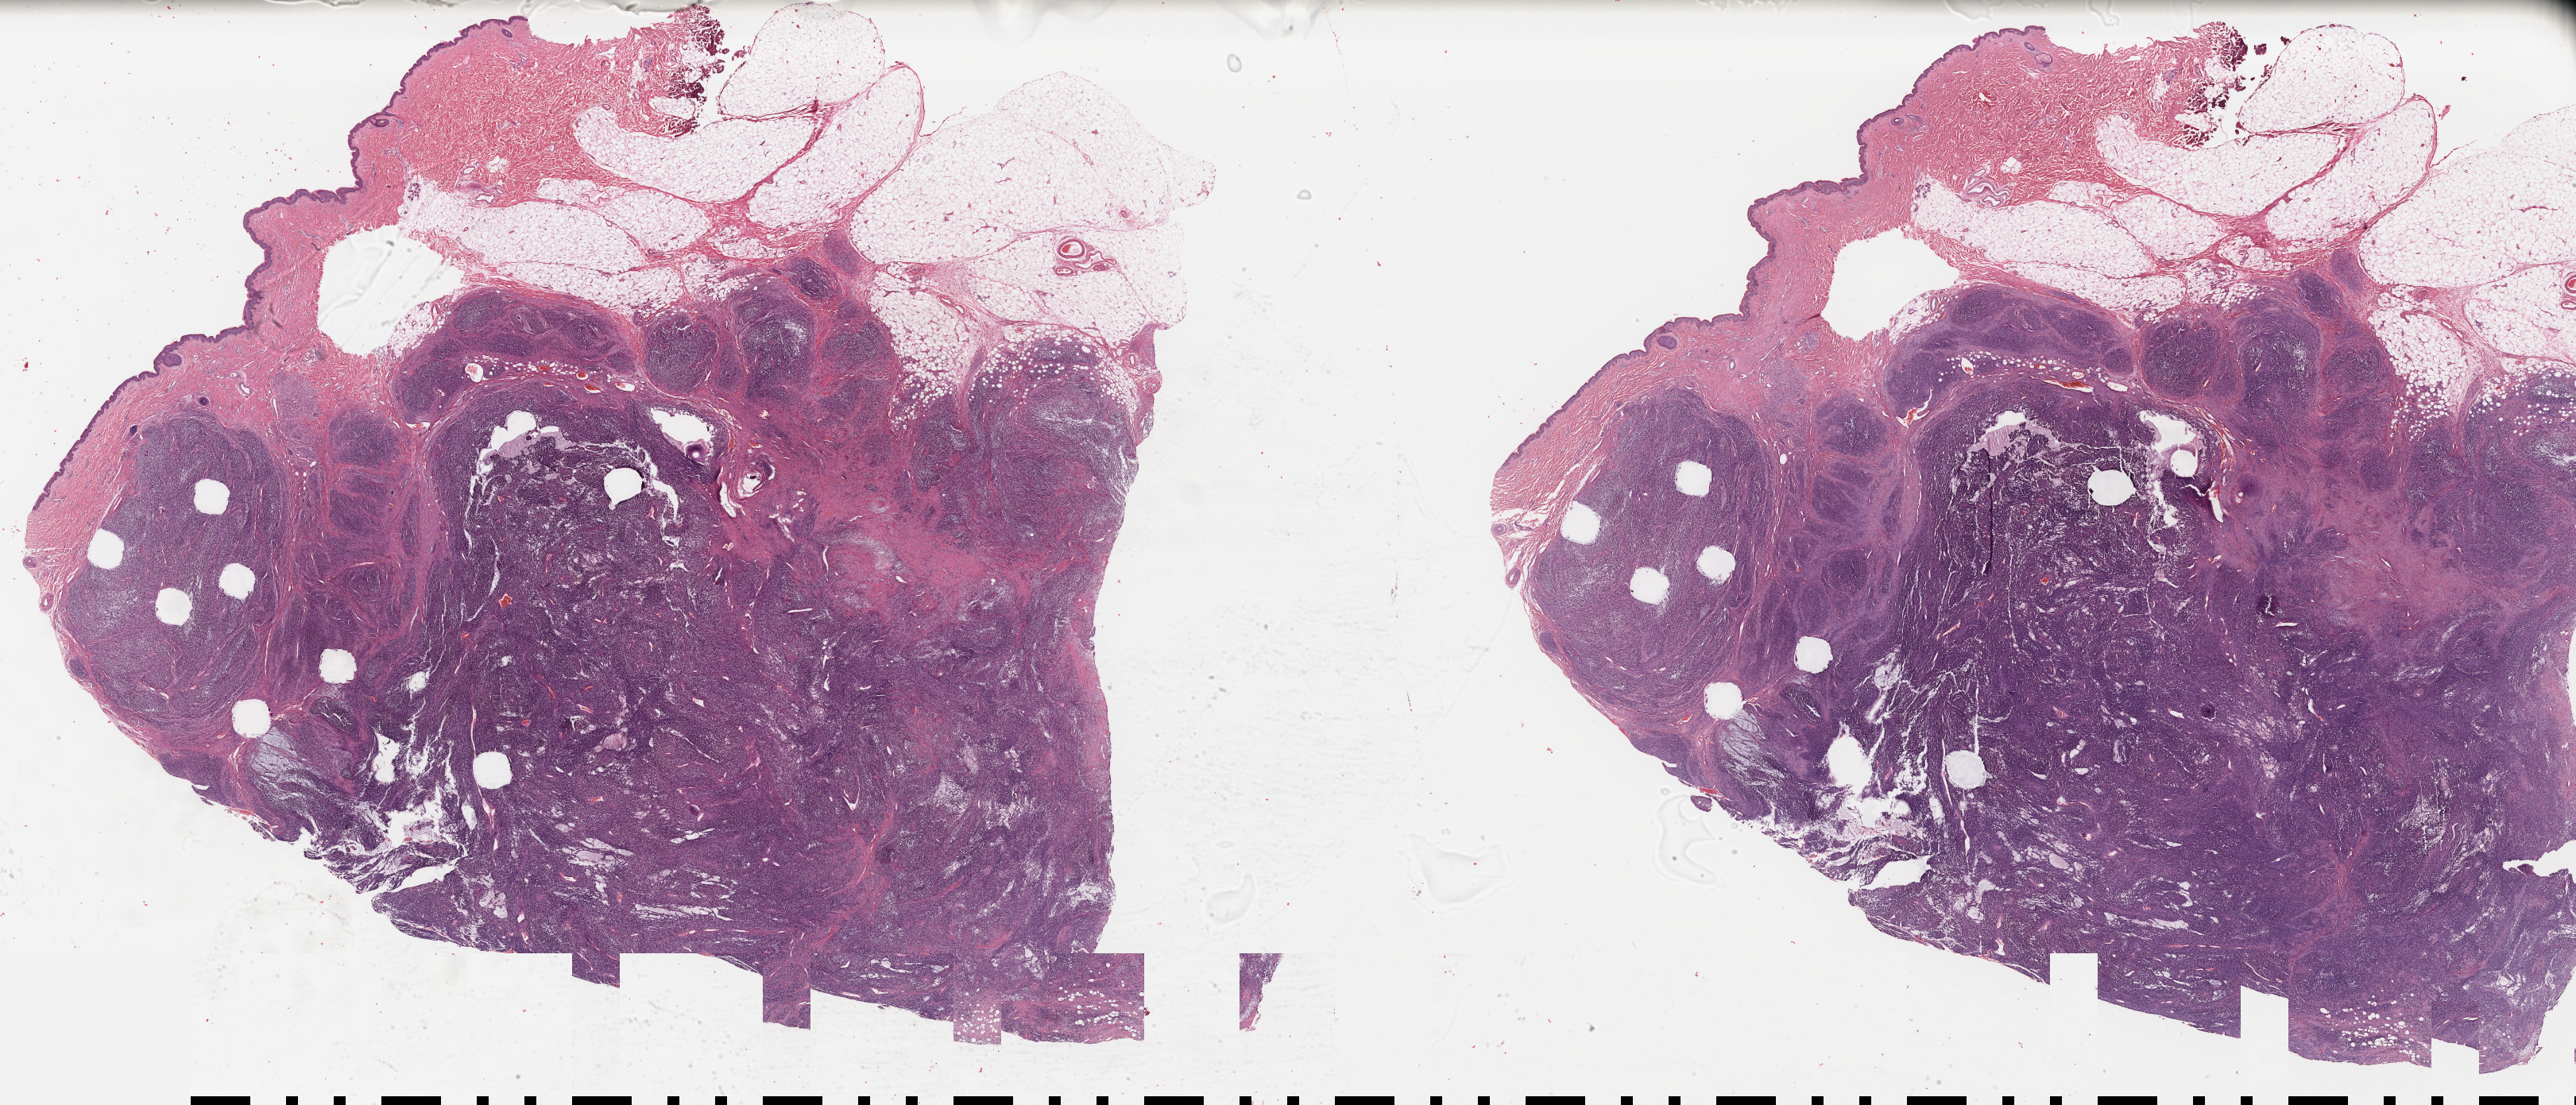
H&E-stained whole-slide image, low-resolution overview of the scanned area, about 51.0 x 21.9 mm (acquisition: 40x scan). FFPE section. Metastatic tumour sample, sampled site: lymph node. Male, age 63 years at initial diagnosis.
This section: metastatic tumour tissue. Patient diagnosis: Malignant melanoma, NOS.